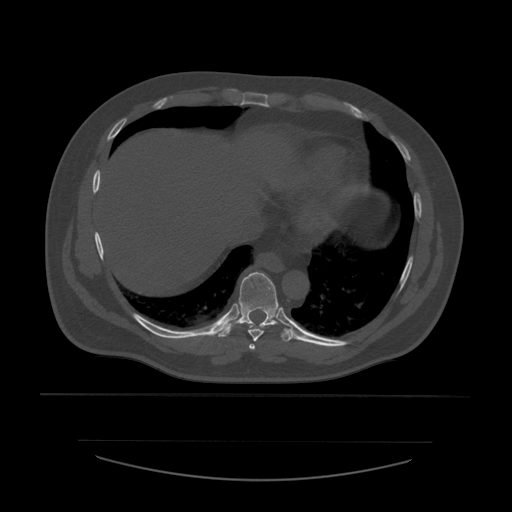
CT including the spine, one axial slice. Reconstruction kernel STANDARD. 120 kVp. Bone window (W 1800 / L 400 HU). 1.25 mm slice thickness. 512 × 512 image matrix, field of view 441 × 441 mm. Patient age 44 years. From the clinical record (not read from this slice): primary cancer: soft tissue sarcoma.
Outlined on this slice (semi-automatically segmented with operator editing):
- T7 vertebra: box from (x=249, y=344) to (x=256, y=350) px
- T8 vertebra: (x=248, y=324)–(x=265, y=342)
- T9 vertebra: (x=218, y=272)–(x=293, y=342)